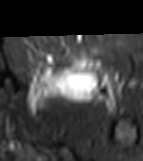
MRI of an extremity soft-tissue mass, one axial slice; slice 43 of 81 in the series (ordered by position); STIR; MR volume resampled by the dataset authors to the PET/CT grid (not the native acquisition matrix); 3.27 mm slice thickness; 143 × 161 image matrix, field of view 140 × 157 mm. Female patient. From the clinical record (not read from this slice): histological type: myxofibrosarcoma; grade: intermediate; site of the primary tumour: left thigh.
Annotated regions visible in this slice (expert contour drawn on MRI and transferred to this co-registered scan by the dataset authors):
- gross tumour volume including surrounding oedema: box from (x=24, y=60) to (x=121, y=111) px
- gross tumour volume (mass): (x=42, y=60)–(x=95, y=95)